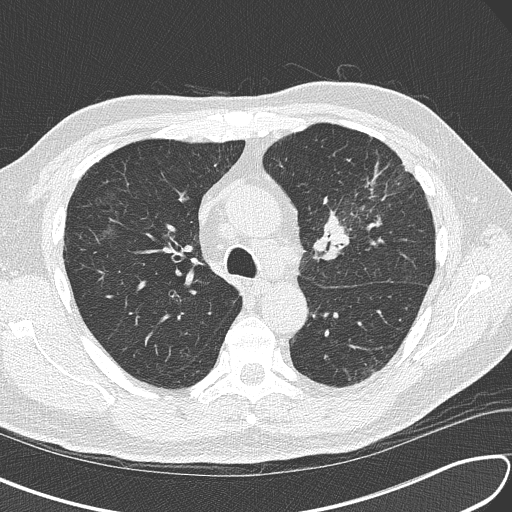
Low-dose screening chest CT, axial slice. Third annual screen. Lung window (W 1500 / L -600 HU). 2 mm slice thickness. Lung (sharp) reconstruction kernel (B50f). Slice 51 of 156 in the series. 512 × 512 image matrix. Male, age 67 years at enrolment.
Expert reader's lesion annotation, box from (x=299, y=178) to (x=400, y=274) px. The exam's reader record, not a measurement of the box and not confirmed to be the same lesion: non-calcified nodule or mass ≥4 mm, left upper lobe, 30 × 23 mm, soft tissue attenuation, pre-existing on the prior screen: no. Lung cancer was diagnosed 41 days after this screen: small cell carcinoma, NOS, left upper lobe, stage IV (AJCC 6th edition), 30 mm at pathology.